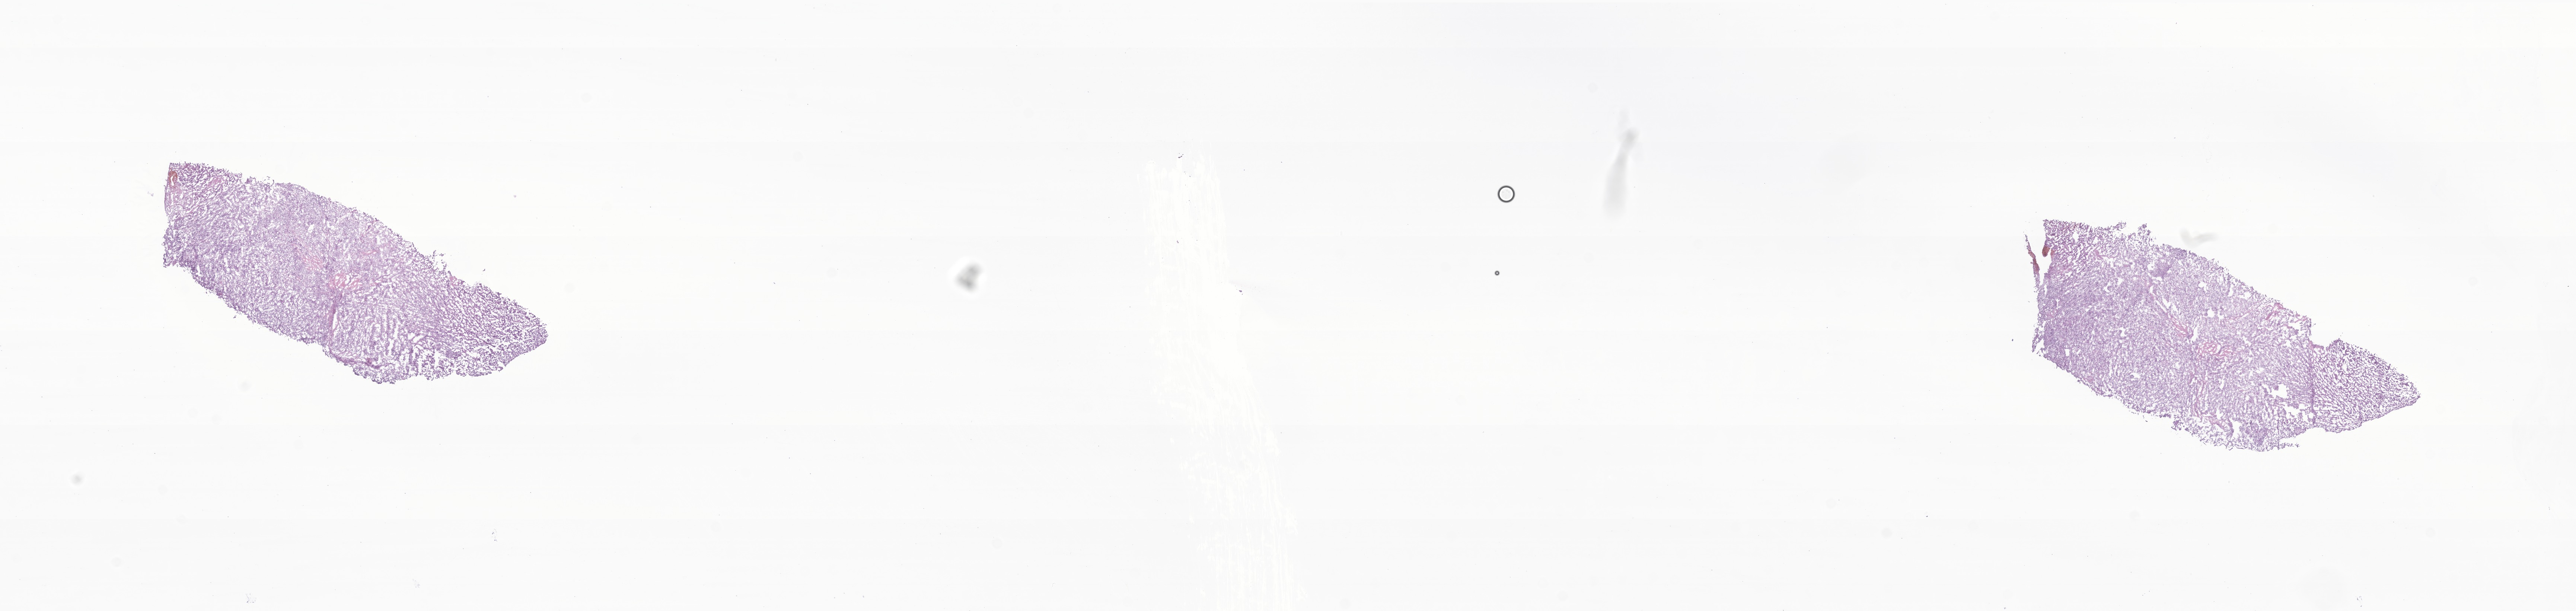
Digitized haematoxylin and eosin-stained section of tumor tissue from the brain, a low-resolution overview of the entire scanned area, about 29.2 x 6.9 mm. Frozen section (OCT-embedded). Patient male; age 230 months (19 years 2 months).
- diagnosis (ICD-O-3 morphology term): Meningioma, NOS